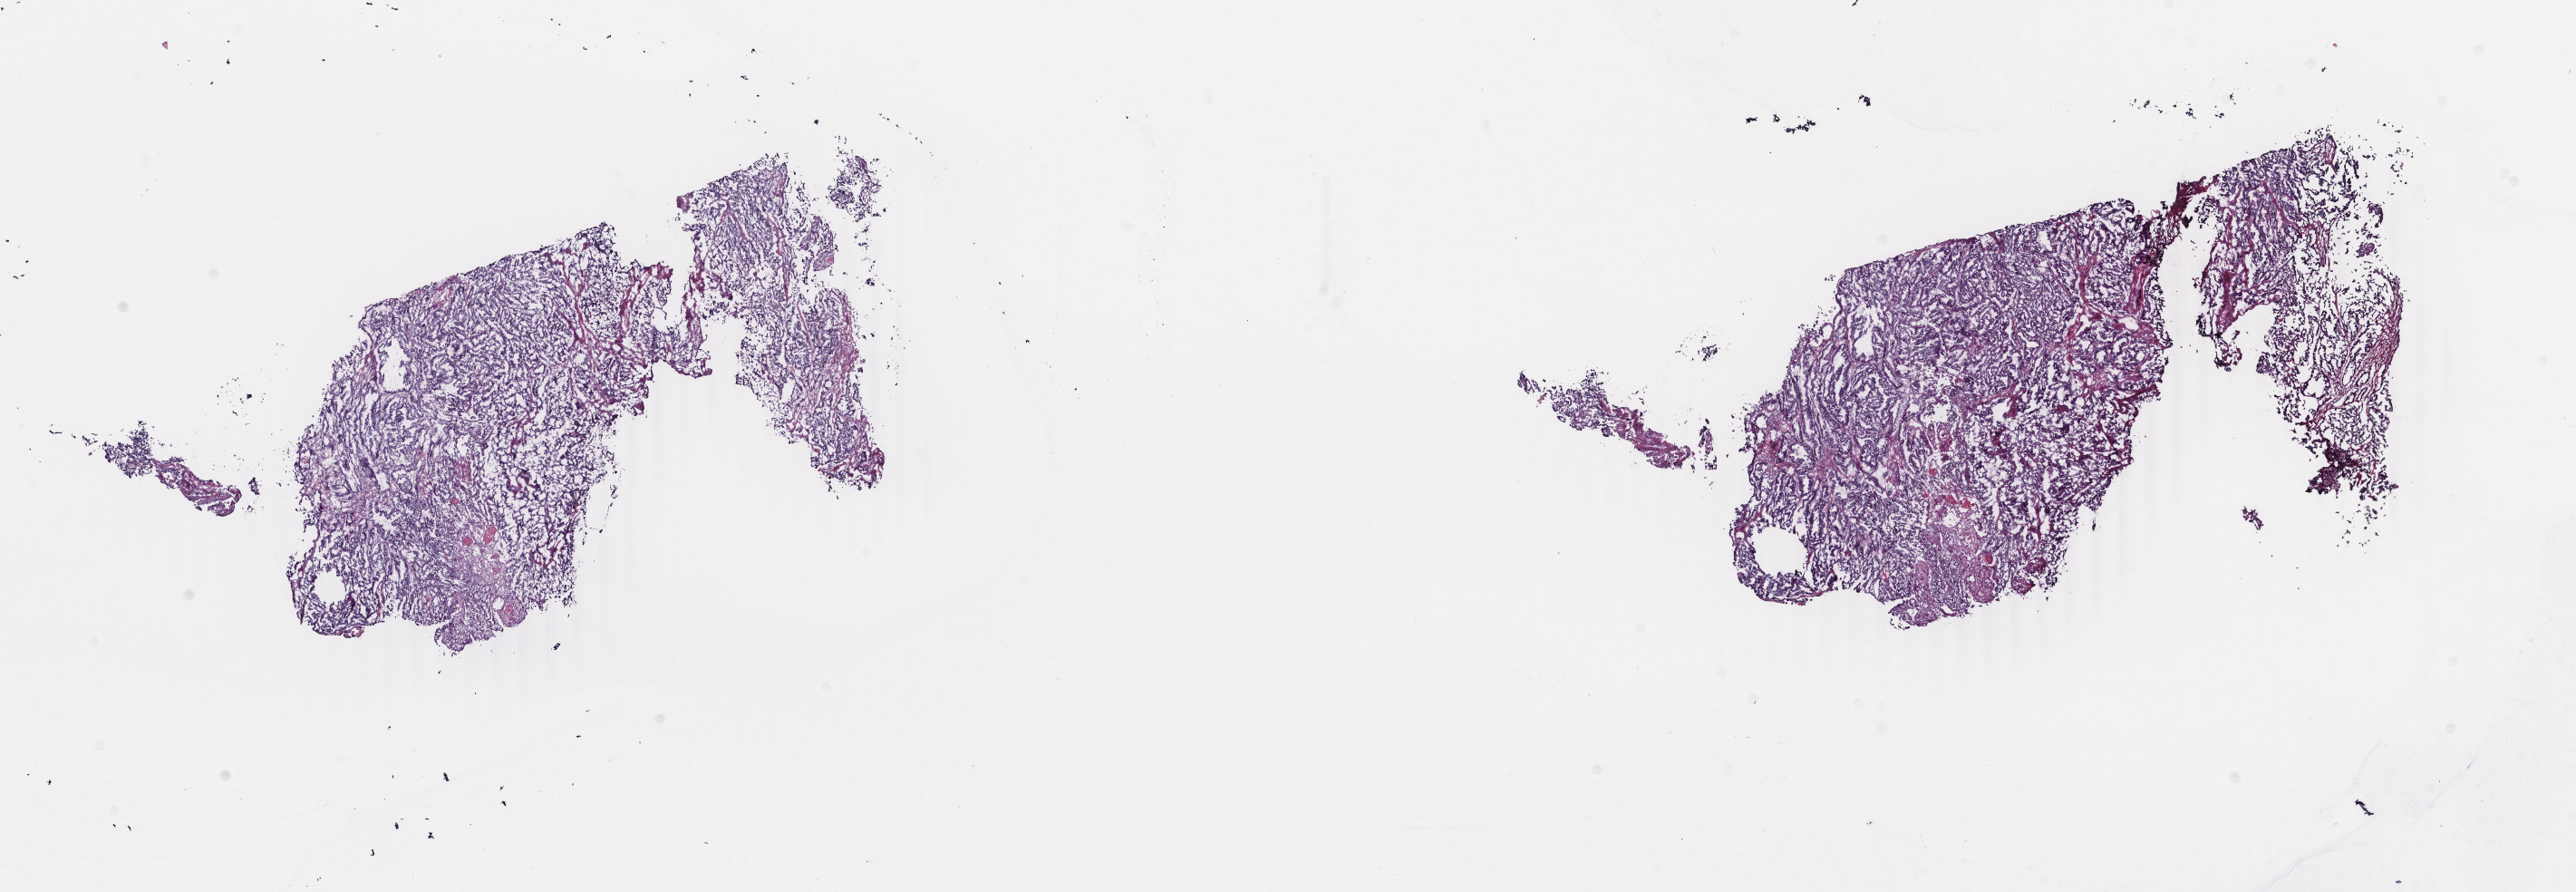
Whole-slide histology image, H&E — a low-resolution overview of the entire scanned area, about 22.6 x 7.8 mm (acquisition: 40x scan), frozen section from the top of the tissue portion, uterus, primary tumour sample. Patient: female, age at initial diagnosis 61 years. Histologic grade: G1 (well differentiated). Composition of this section per pathologist review: tumour cells 100%, tumour nuclei 90%, normal cells 0%, stromal cells 0%, necrosis 0%. Inflammatory infiltration, as recorded: lymphocyte infiltration 0%, monocyte infiltration 0%, neutrophil infiltration 0%.
FIGO stage: IA. Pathologic diagnosis: Endometrioid adenocarcinoma, NOS (endometrium).